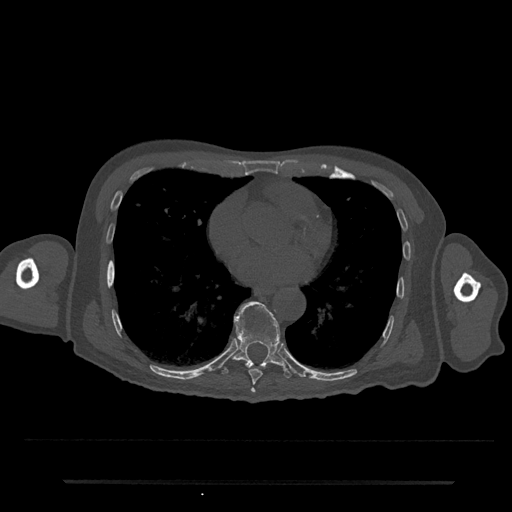
CT including the spine, one axial slice. Slice 391 of 797 in the series (ordered by position). Reconstruction kernel Br40s/3. 120 kVp. Bone window (W 1800 / L 400 HU). 512 × 512 image matrix. Patient: male, 74 years. Case-level facts recorded for this patient, not image findings: primary cancer: prostate.
Structures marked on this image (semi-automatically segmented with operator editing):
- T7 vertebra: bounding box <250,388,256,393> (left, top, right, bottom; pixels)
- T8 vertebra: <249,369,262,385>
- T9 vertebra: <222,301,292,379>